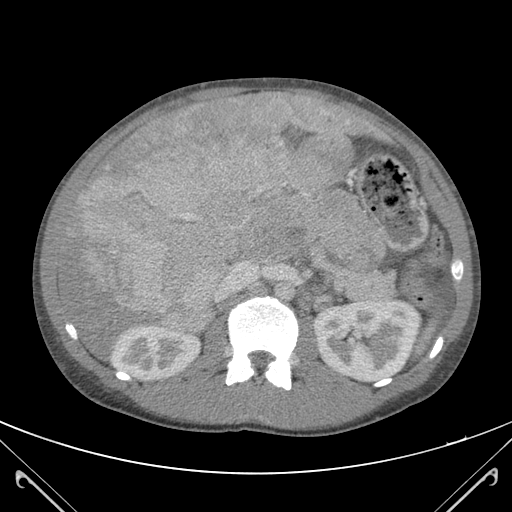
Contrast-enhanced abdominal CT (liver protocol), one axial slice. Slice 66 of 118 in the series (ordered by position). 120 kVp. Soft-tissue window (W 400 / L 40 HU). 3 mm slice thickness. 512 × 512 image matrix. Case-level facts recorded for this patient, not image findings: diagnosis: hepatocellular carcinoma (patient treated with transarterial chemoembolisation; whether this scan precedes or follows treatment is not stated here); TNM stage (as recorded): Stage-IIIB; Child-Pugh class: A; tumour nodularity: uninodular.
Outlined on this slice (semi-automatic segmentation, software-assisted and operator-edited):
- abdominal aorta: bounding box [x1, y1, x2, y2] px = [275, 279, 295, 302]
- liver parenchyma outside the tumour (the mass and vessels are separate outlines, so this box may not span the whole liver): [58, 93, 362, 356]
- mass: [60, 93, 364, 333]
- liver vessels: [215, 259, 268, 302]